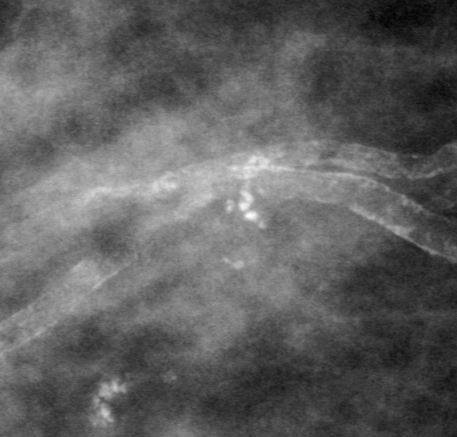
Crop from a digitized film mammogram around one marked abnormality, right breast, MLO view, BI-RADS breast density category 3 (scale 1–4).
Marked abnormality: calcifications, morphology coarse, distribution clustered; BI-RADS assessment category 0 (incomplete: needs additional imaging); pathology (as recorded): benign.